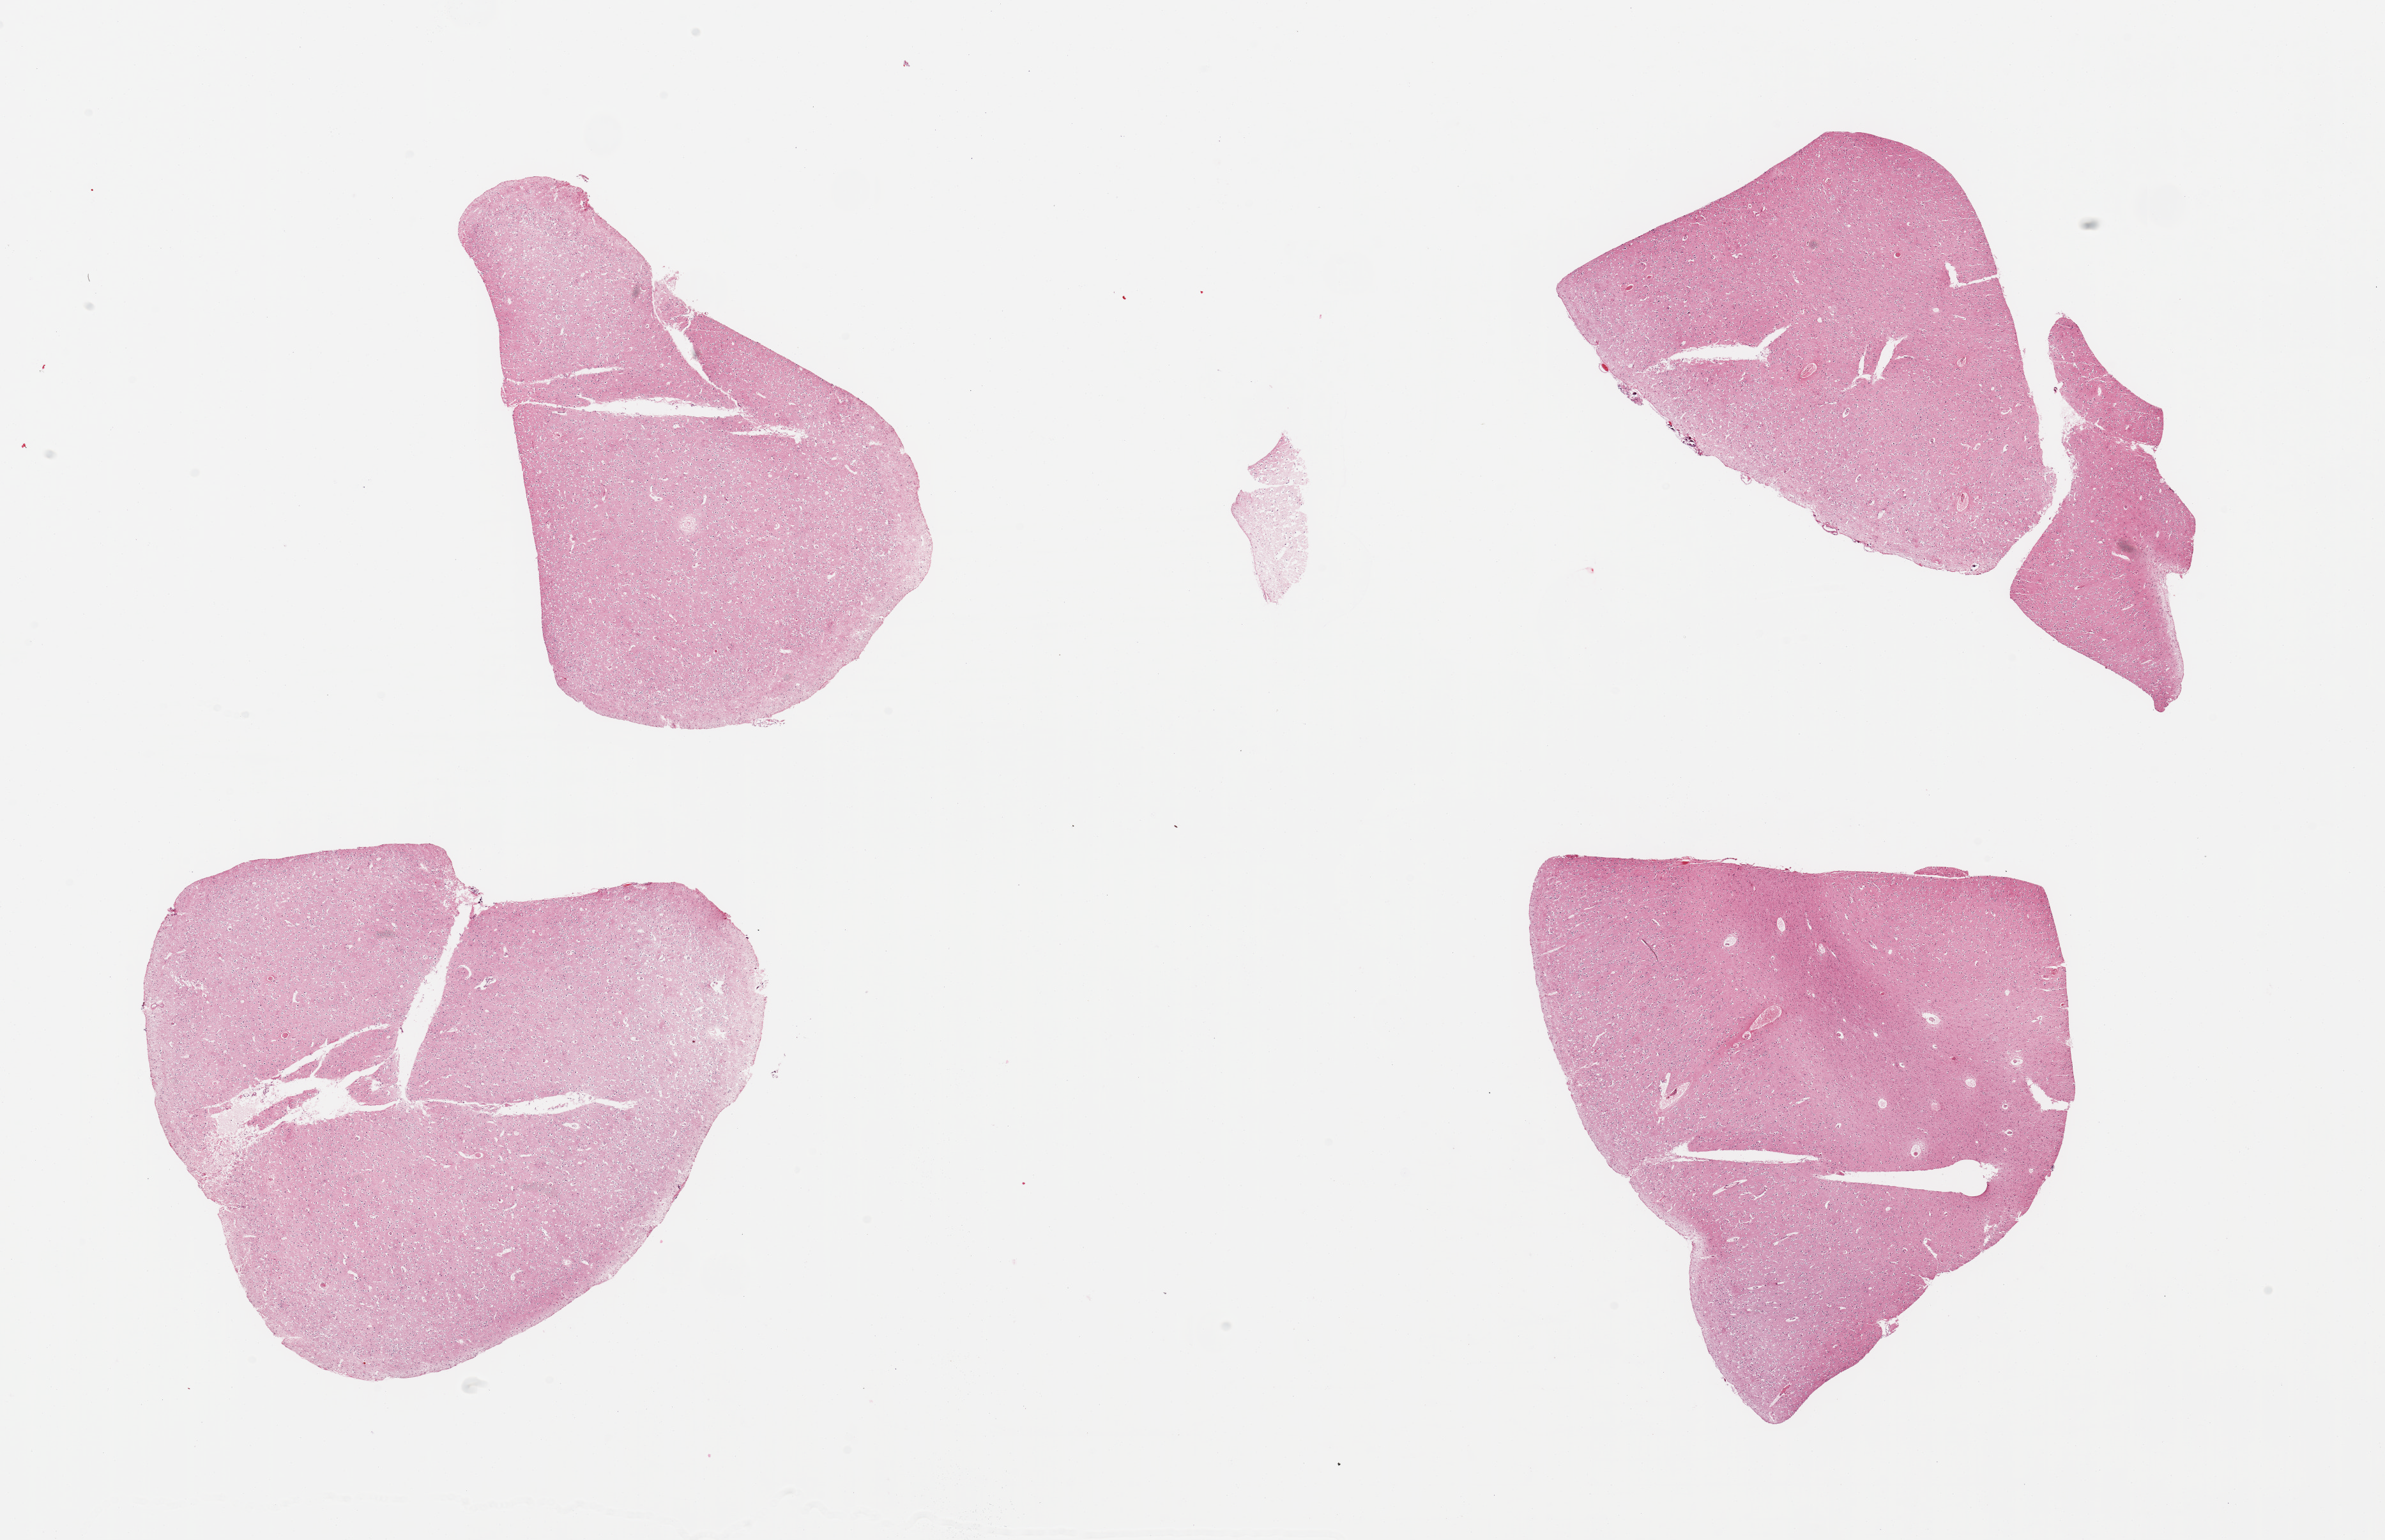
Whole-slide image, H&E stain, a low-resolution overview of the entire scanned area, about 29.5 x 19.1 mm (from a 20x scan). PAXgene-fixed paraffin-embedded (PFPE) section. Target tissue: cerebral cortex. Tissue donor sample. Donor sex: male.
* review note (as recorded): 4 pieces; questionable increase in glial cells